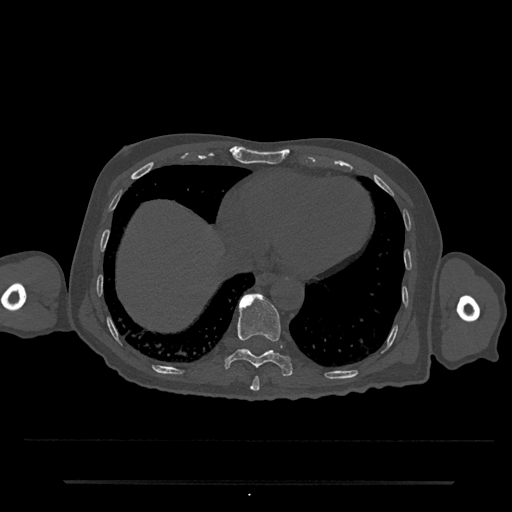
CT including the spine, one axial slice; slice 313 of 797 in the series (ordered by position); 120 kVp; bone window (W 1800 / L 400 HU); 0.5 mm slice thickness; 512 × 512 image matrix, field of view 427 × 427 mm. Male patient, age 74 years. Case-level facts recorded for this patient, not image findings: primary cancer: prostate.
Structures marked on this image (semi-automatically segmented with operator editing):
- T10 vertebra: box from (x=224, y=293) to (x=293, y=377) px
- T9 vertebra: (x=250, y=376)–(x=260, y=391)